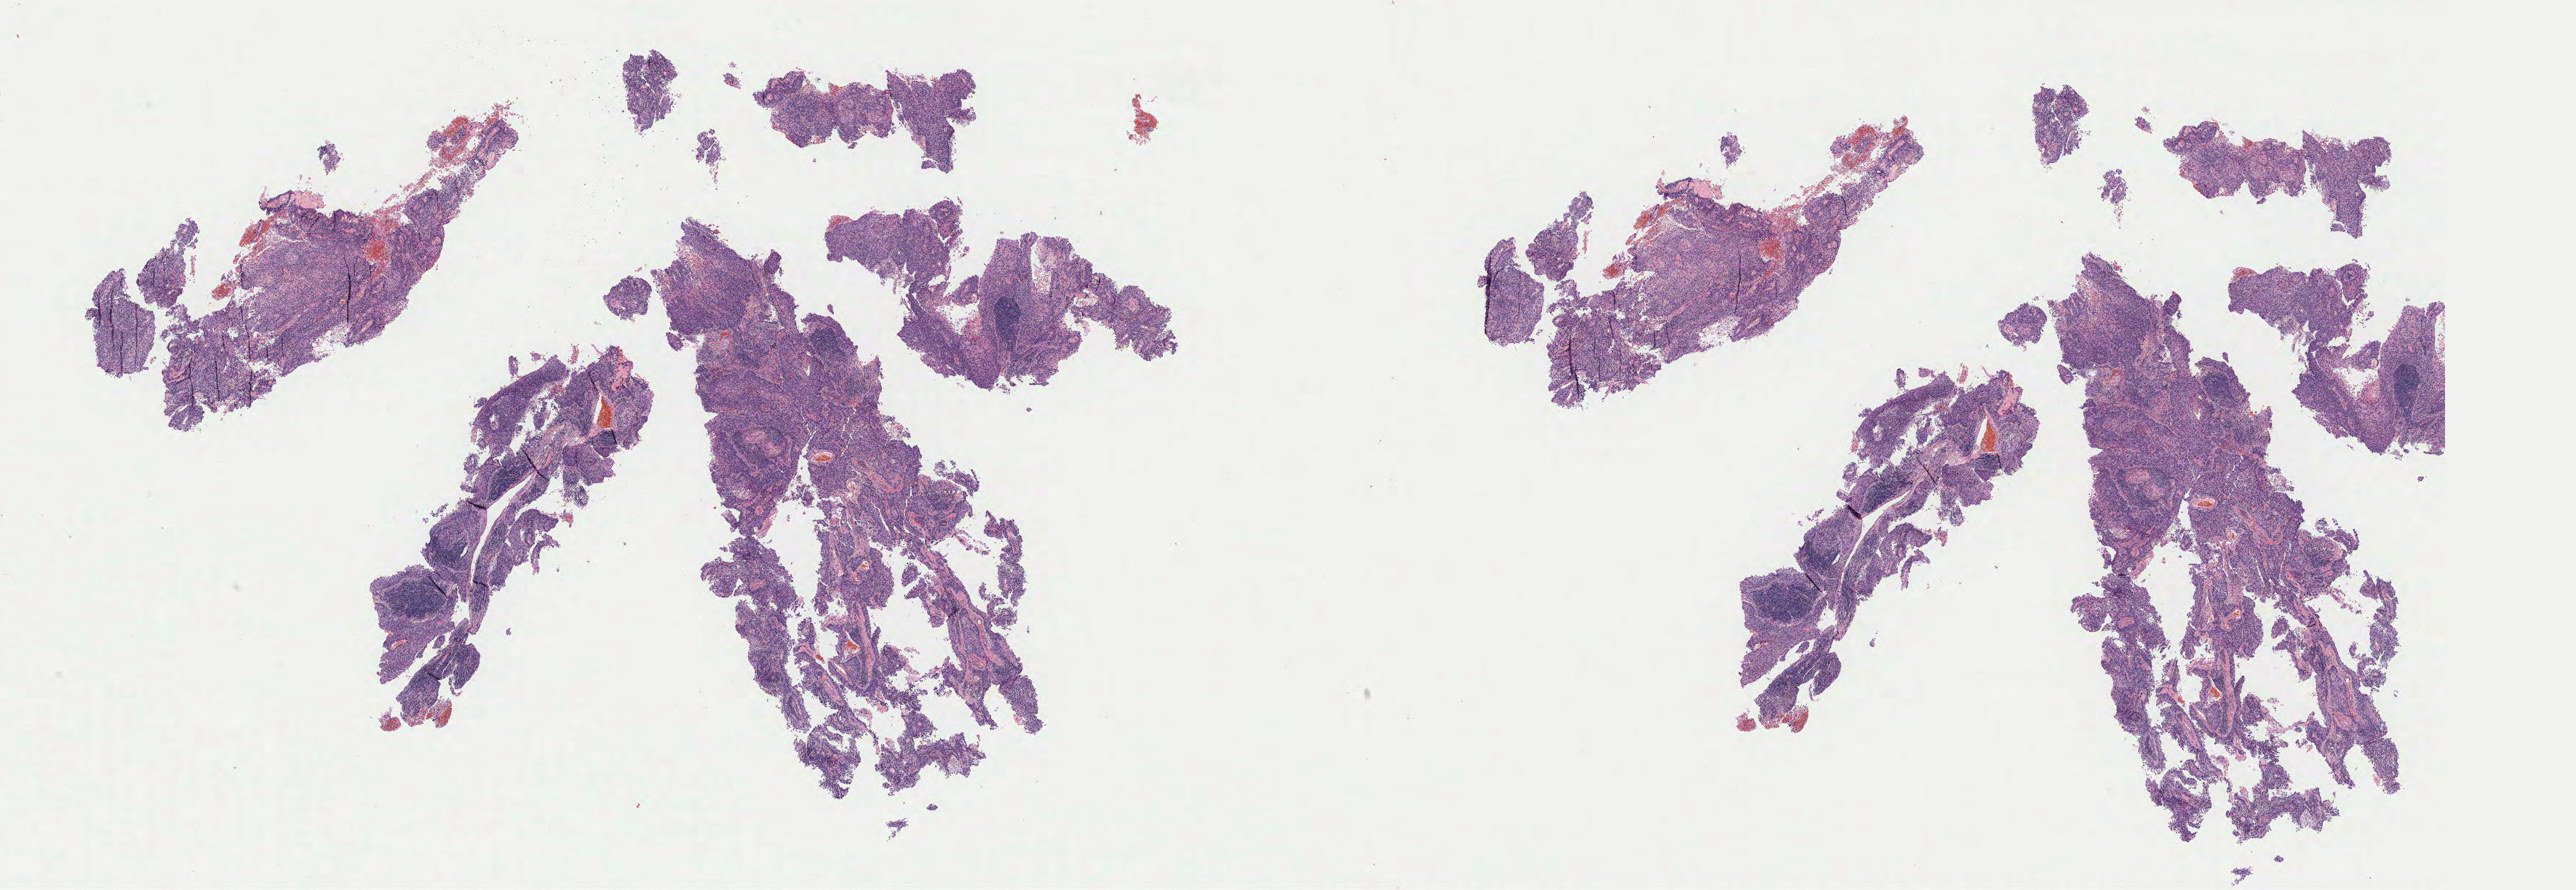
Whole-slide image, haematoxylin and eosin stain, a low-resolution overview of the entire scanned area, about 28.1 x 9.7 mm. Tumor tissue. Site: cervix. Patient female; 58 years old.
• histologic diagnosis: Squamous cell carcinoma, keratinizing, NOS